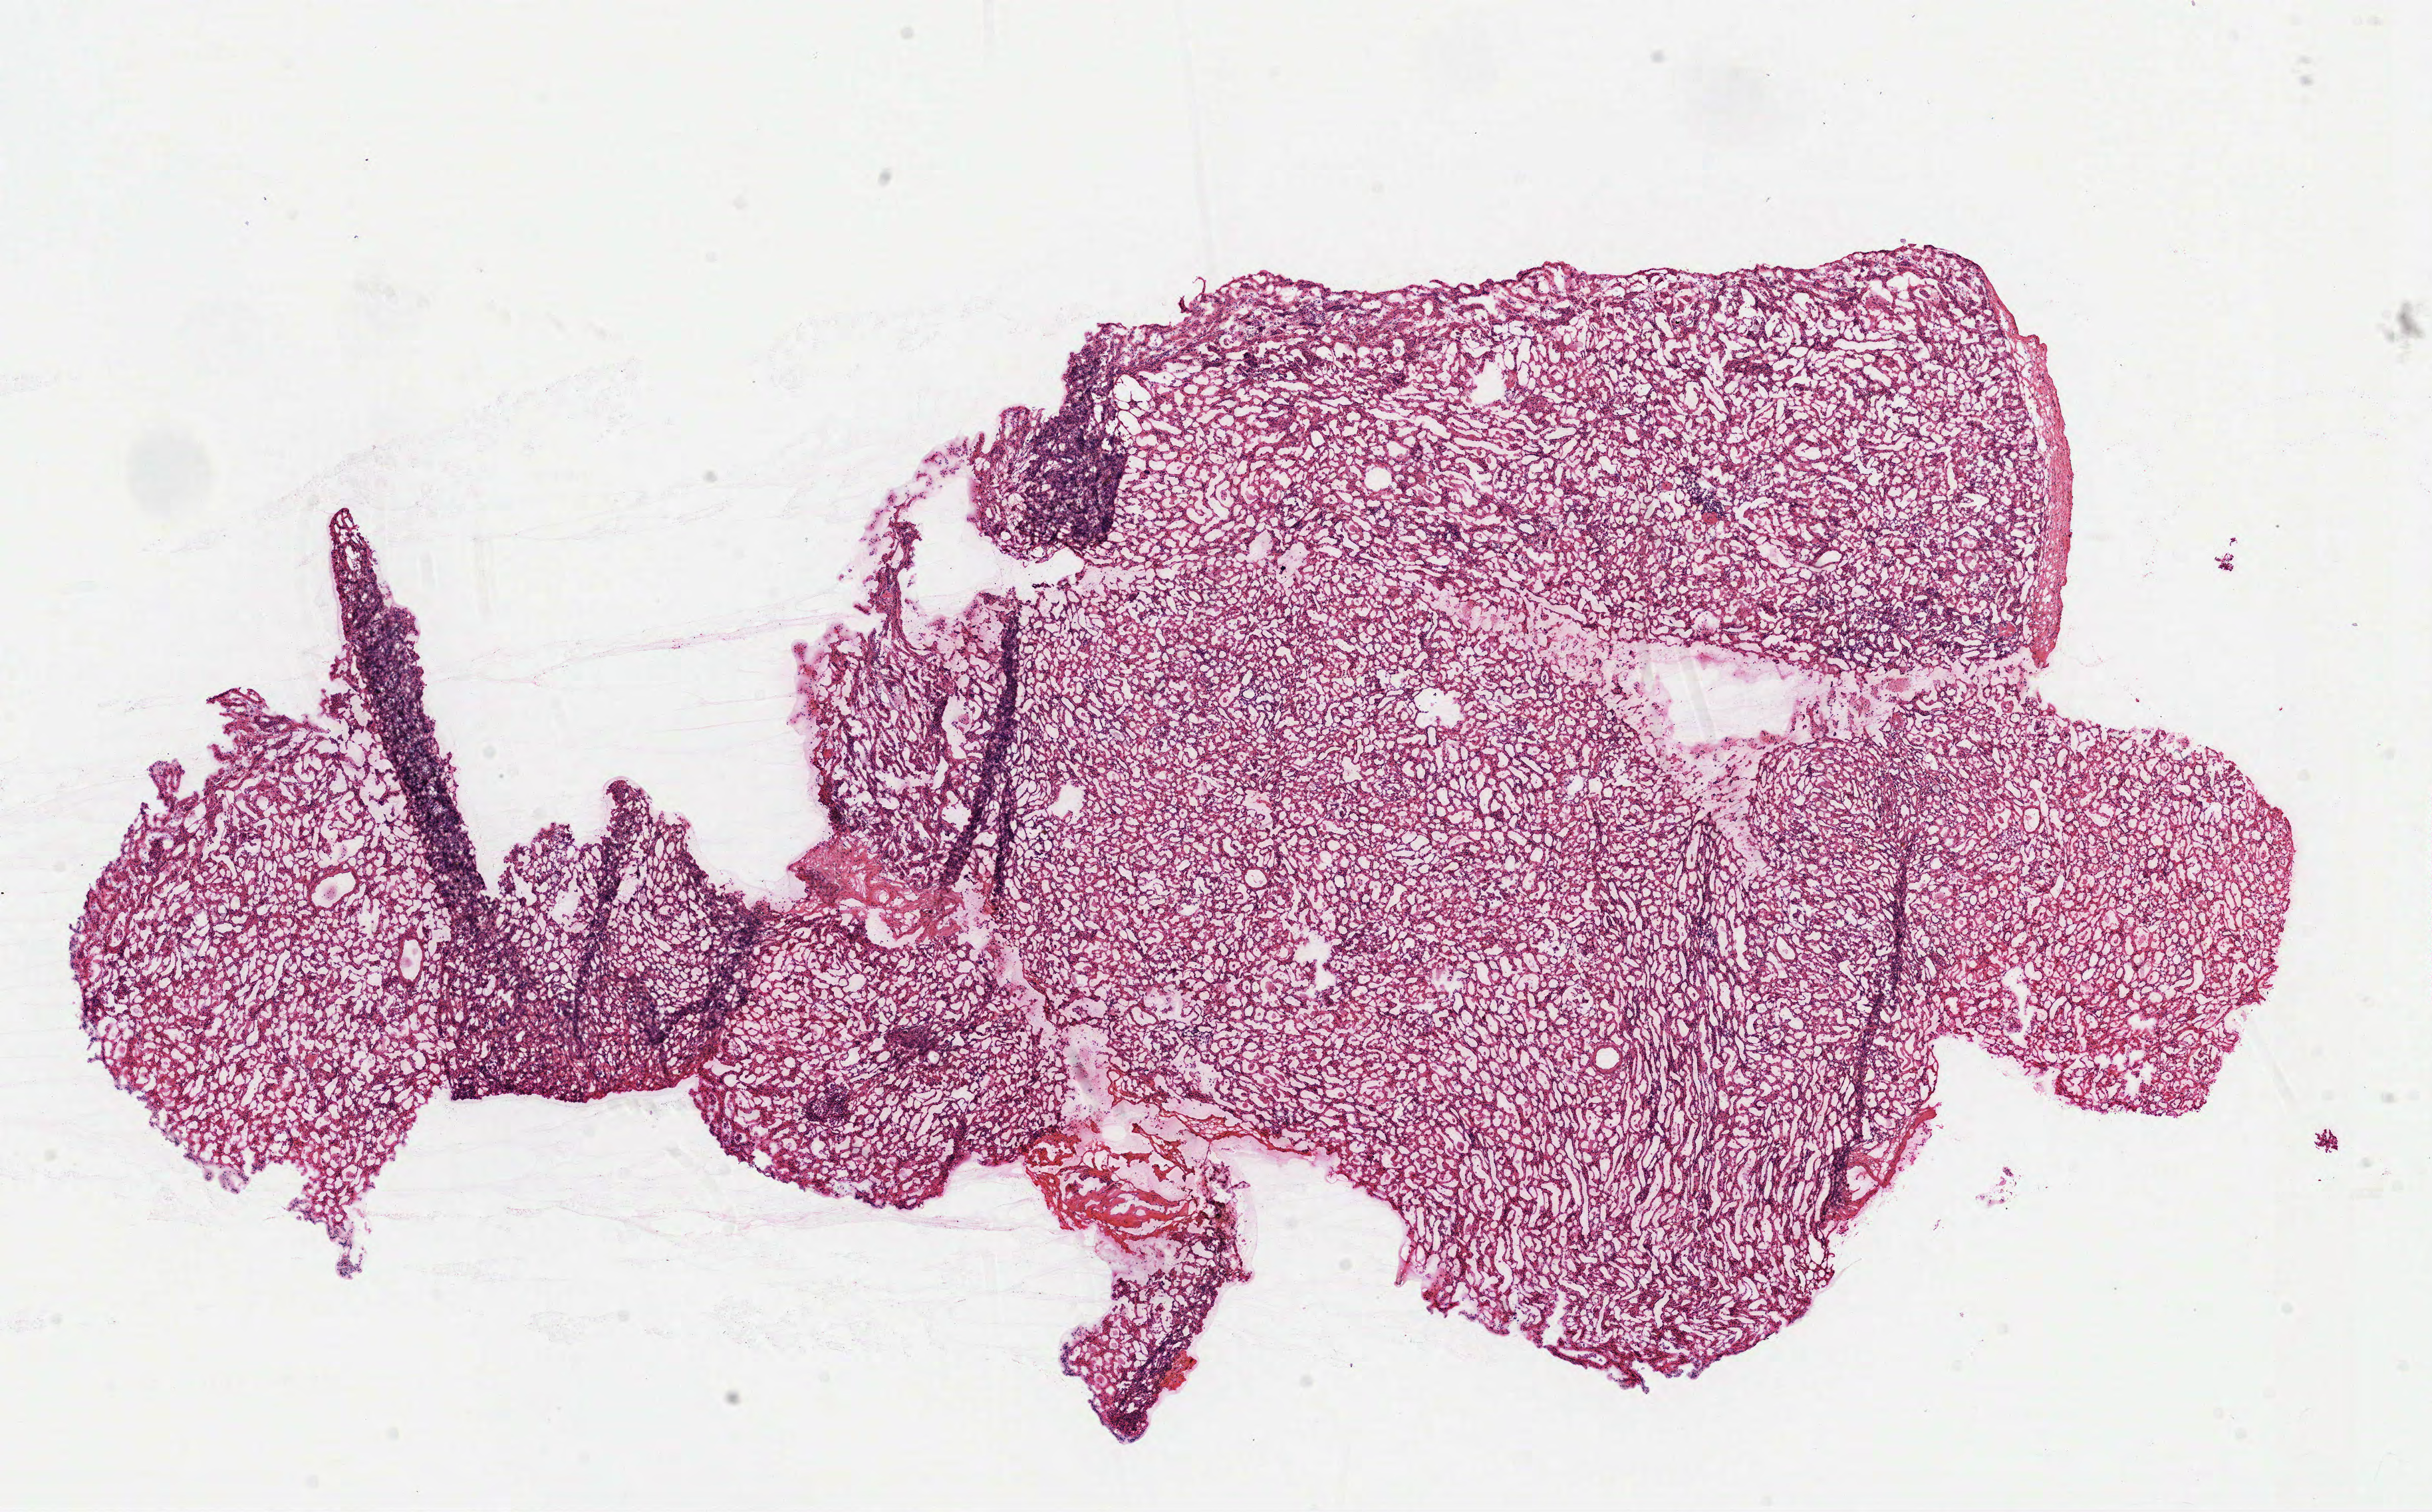
Digitized H&E-stained tissue section (whole slide) — low-resolution overview of the scanned area, about 14.7 x 9.2 mm (acquisition: 40x scan), frozen section from the top of the tissue portion, sample: solid tissue normal (non-tumour tissue), kidney. Female patient; age at initial diagnosis 54 years.
• this section: solid tissue normal (non-tumour) sample from the same patient
• patient diagnosis: Clear cell adenocarcinoma, NOS